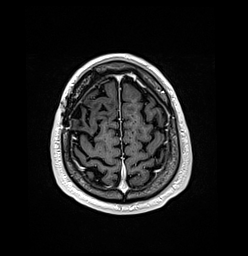
Brain MRI from a brain-tumour surgery series, one axial slice; position 30 of 176 along the scan axis; T1-weighted post-contrast; 1 mm slice thickness; 248 × 256 image matrix, field of view 242 × 250 mm. Case-level facts recorded for this patient, not image findings: histopathology: Oligodendroglioma; WHO grade: 3; IDH mutation: yes.
Structures marked on this image (outlined manually by an expert reader):
- previous resection cavity: bounding box [x1, y1, x2, y2] px = [71, 104, 83, 126]